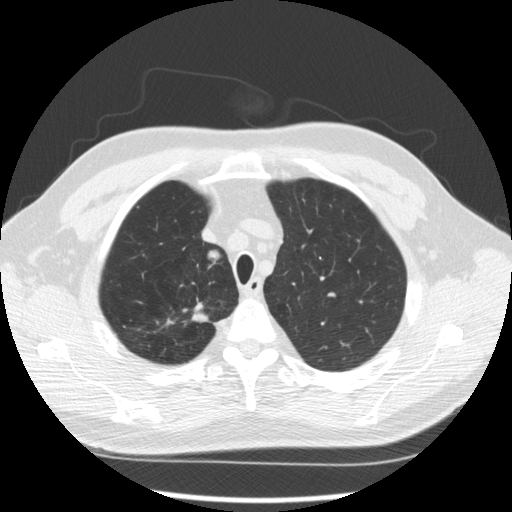
Low-dose screening chest CT, axial slice; second screening round (one year after baseline); lung window (W 1500 / L -600 HU); standard (soft-tissue) reconstruction kernel (STANDARD); 512 × 512 image matrix, field of view 360 × 360 mm. Male, age 64 years at enrolment.
2 lesions marked by an expert reader on this slice (largest first), bounding box (x1, y1, x2, y2) in pixels: (170, 298, 220, 333); (188, 245, 226, 272). The screening reader recorded 3 non-calcified nodules or masses ≥4 mm on this exam (right upper lobe, right upper lobe, right upper lobe); which of them these boxes mark is not recorded. Official screen result: positive, other. Lung cancer was diagnosed 411 days after this screen: adenocarcinoma, NOS, right upper lobe, moderately differentiated (G2), stage IA (AJCC 6th edition), 14 mm at pathology.